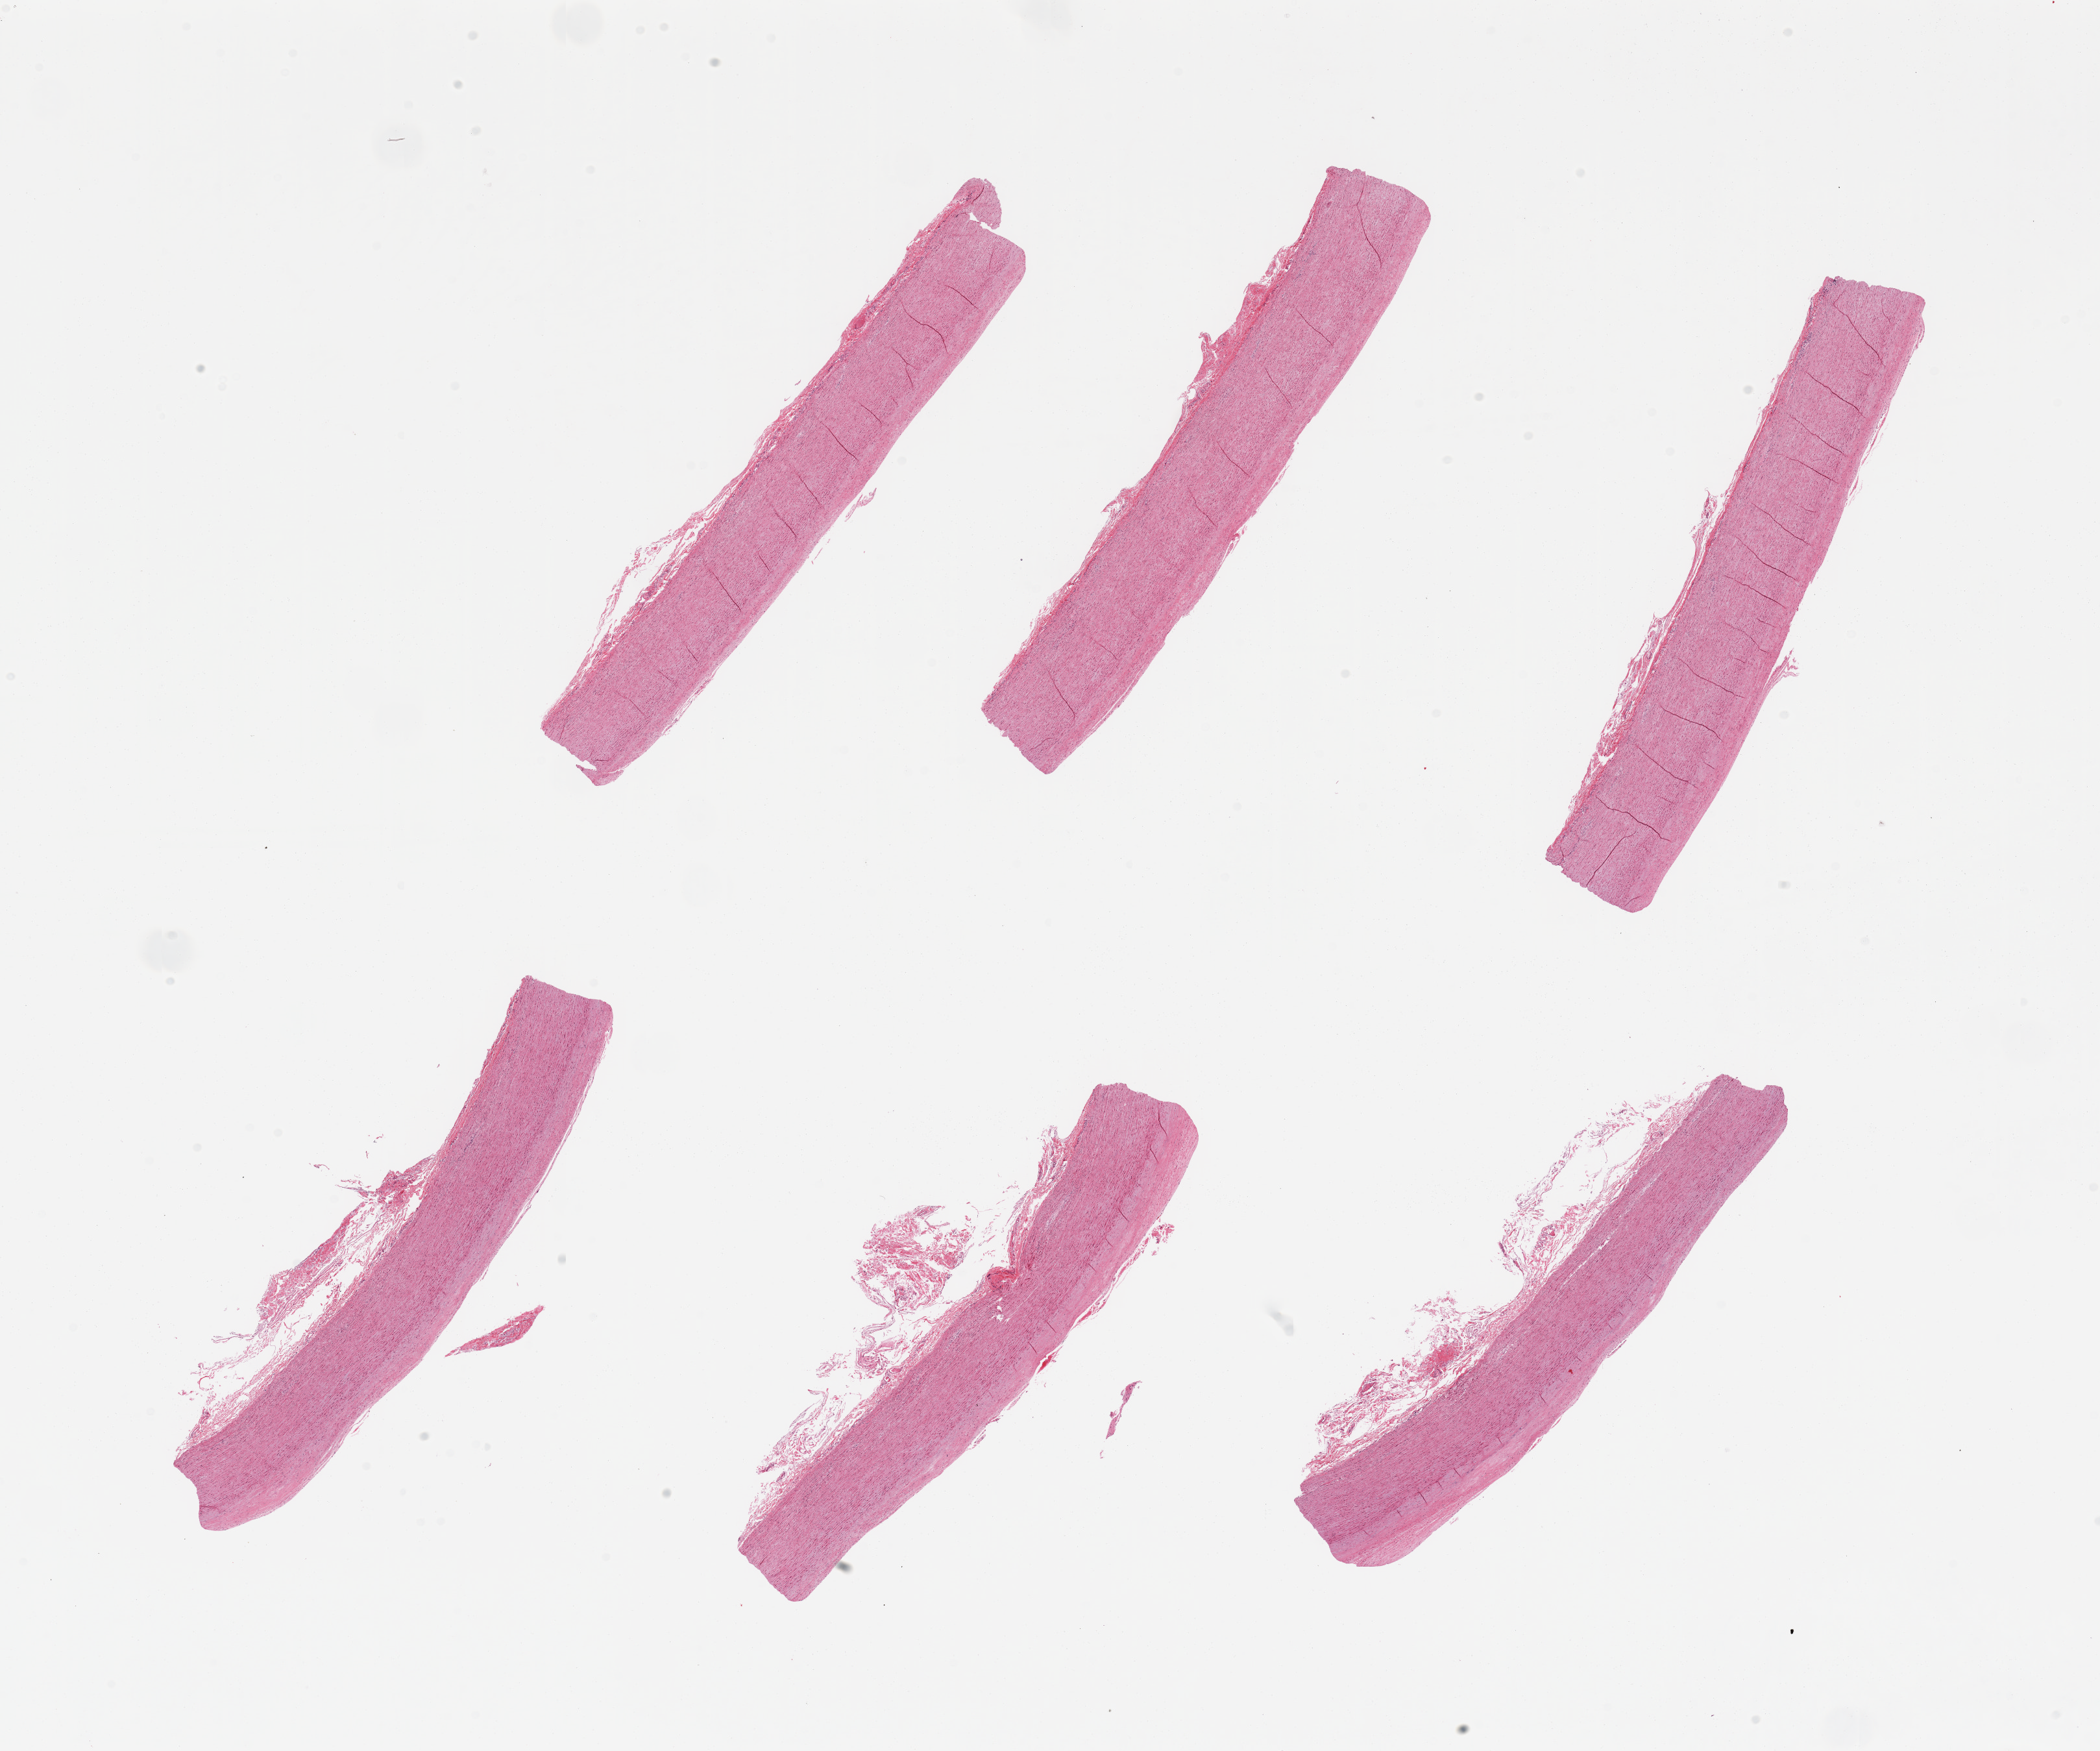
Whole-slide image, H&E stain — shown as a low-resolution overview of the whole scanned area (about 25.6 x 21.3 mm, acquisition: 20x scan), PAXgene-fixed paraffin-embedded (PFPE) section, section of aorta (target tissue), tissue donor sample. Female donor.
Review note (as recorded): 6 pieces; flat plaques.